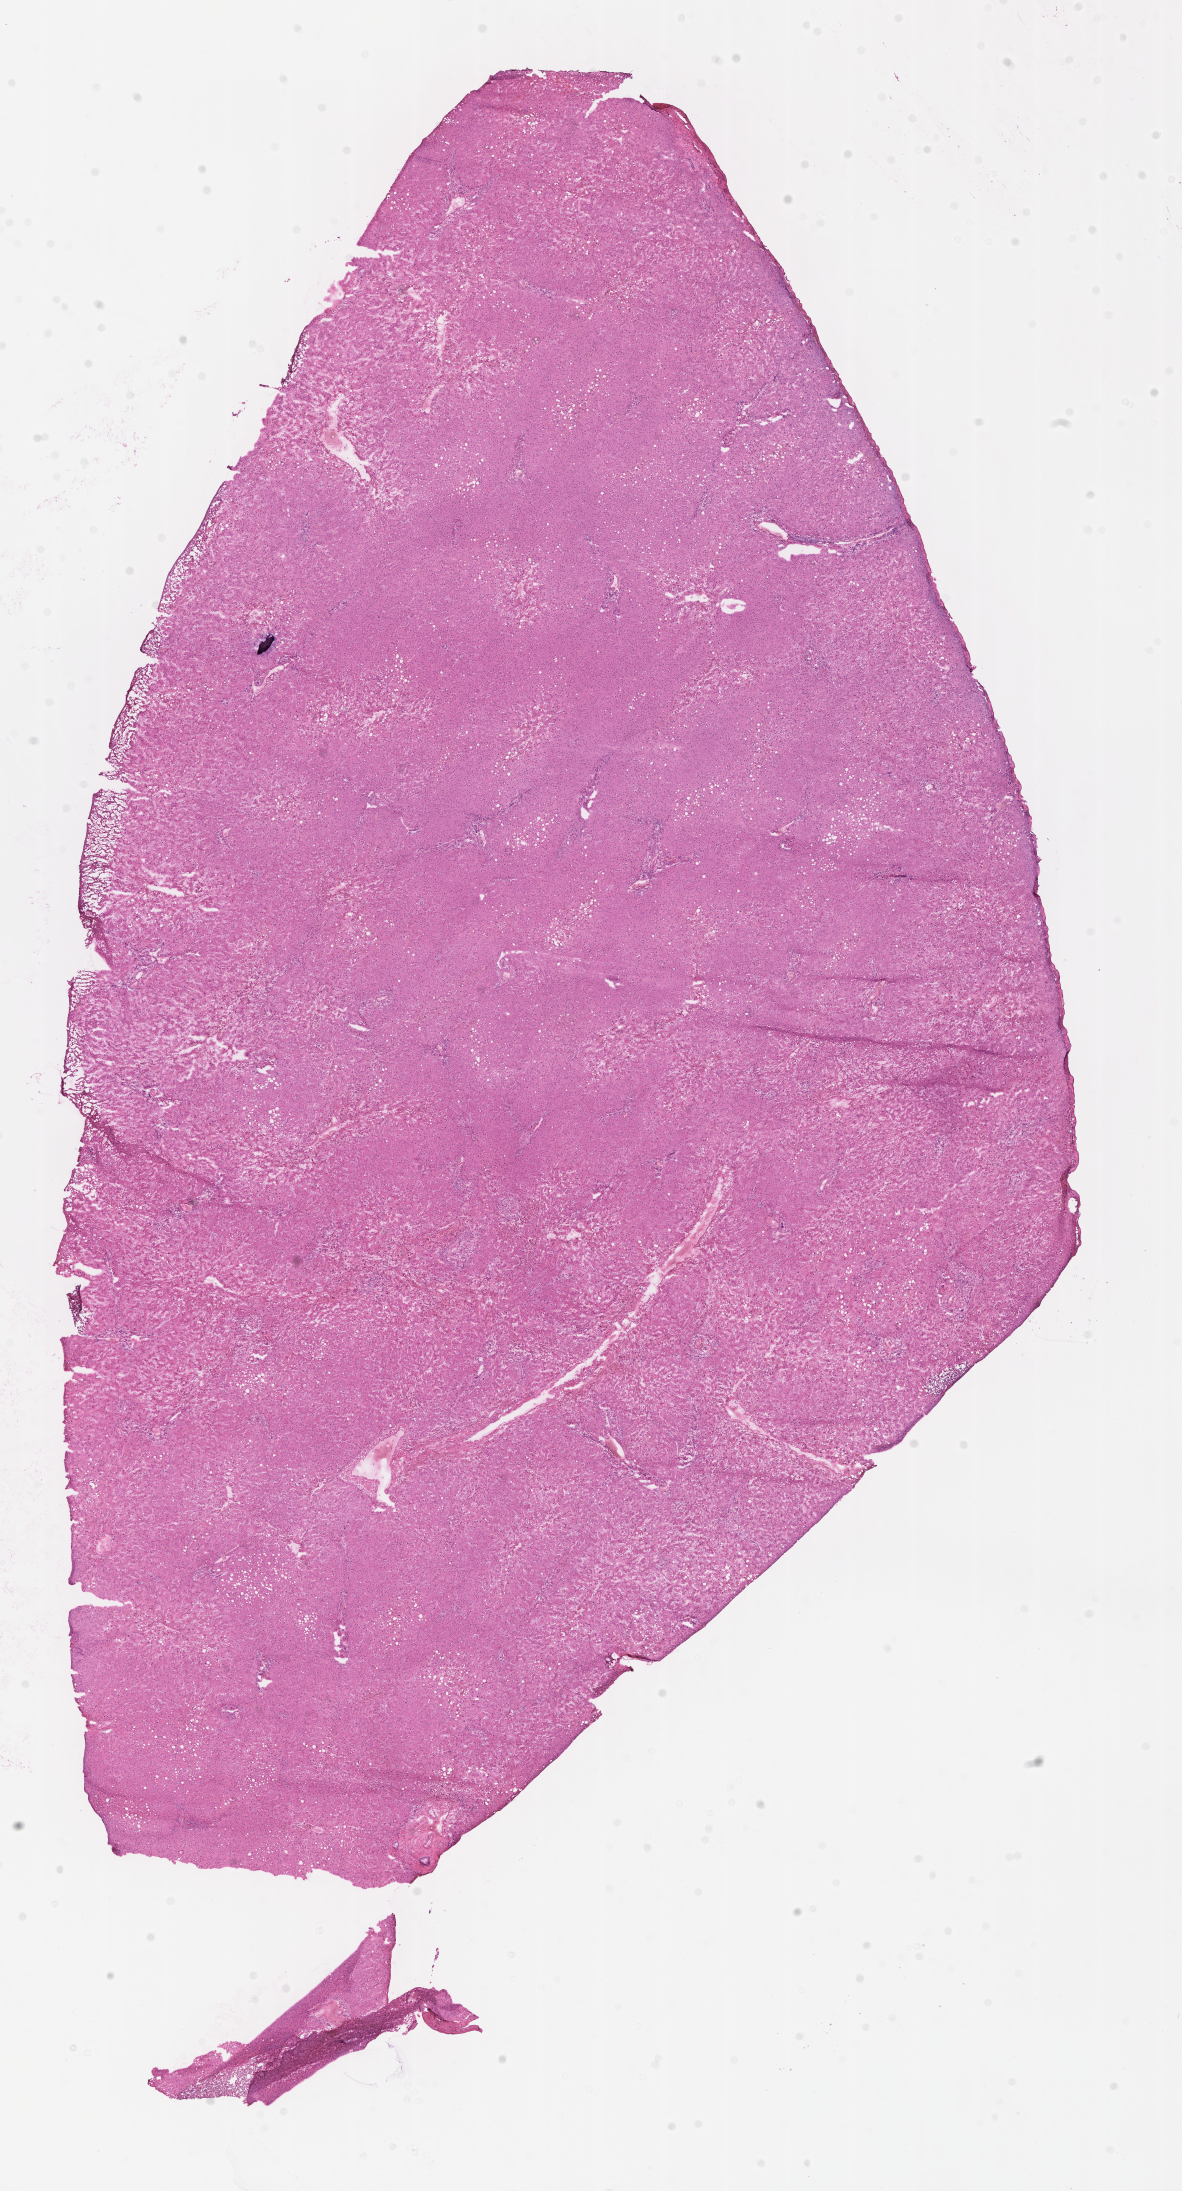
Digitized hematoxylin and eosin (H&E)-stained section, whole scanned area (about 9.6 x 17.7 mm) shown as a low-resolution overview, frozen section, specimen: normal-tissue sample (non-tumor) from a patient with adenocarcinoma, NOS, site: rectum. Patient: male, age at initial diagnosis 34 years. Composition of this section per pathologist review: tumor cells 0%, tumor nuclei 0%, stromal cells 0%, necrosis 0%, normal cells 100%. Inflammatory infiltration, as recorded: lymphocyte infiltration 0%, monocyte infiltration 0%, neutrophil infiltration 0%.
* this section: non-tumor tissue sample; the patient's diagnosis is given above
* section: bottom of the tissue portion